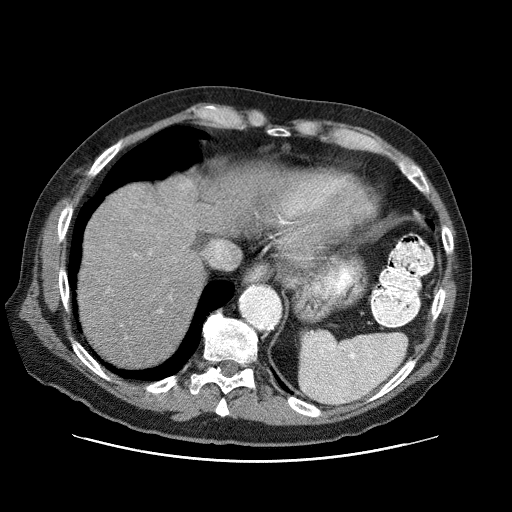
Contrast-enhanced abdominal CT (liver protocol), one axial slice. Position 64 of 87 along the scan axis. 120 kVp. One of 3 acquisitions stored at this slice position. Soft-tissue window (W 400 / L 40 HU). 512 × 512 image matrix. From the clinical record (not read from this slice): diagnosis: hepatocellular carcinoma (patient treated with transarterial chemoembolisation; whether this scan precedes or follows treatment is not stated here); TNM stage (as recorded): Stage-IIIA; Child-Pugh class: A.
Outlined on this slice (semi-automatically segmented with operator editing):
- liver parenchyma outside the tumour (the mass and vessels are separate outlines, so this box may not span the whole liver): box from (x=78, y=172) to (x=266, y=368) px